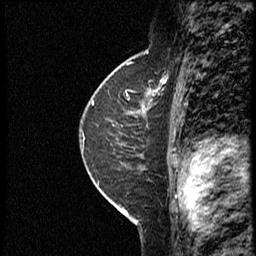
Breast MRI (dynamic contrast-enhanced), one sagittal slice. Position 24 of 40 along the scan axis. Dynamic contrast-enhanced study with each time point stored as its own series, time point 2 of 4 at this slice position (early post-contrast, ordered by acquisition time). 1.5 T. TE 4.2 ms, TR 18.8 ms. 256 × 256 image matrix, field of view 200 × 200 mm. Female patient. Case-level facts recorded for this patient, not image findings: setting: breast cancer imaged before/during neoadjuvant chemotherapy; receptor status: HER2-positive.
Outlined on this slice (semi-automatic segmentation, software-assisted and operator-edited):
- analysis volume of interest (the breast-tissue region the enhancement analysis was run in; not a lesion): box from (x=91, y=79) to (x=170, y=153) px
- tumour enhancement mask (voxels above the 100 % enhancement threshold inside the analysis volume of interest): (x=148, y=89)–(x=155, y=95)